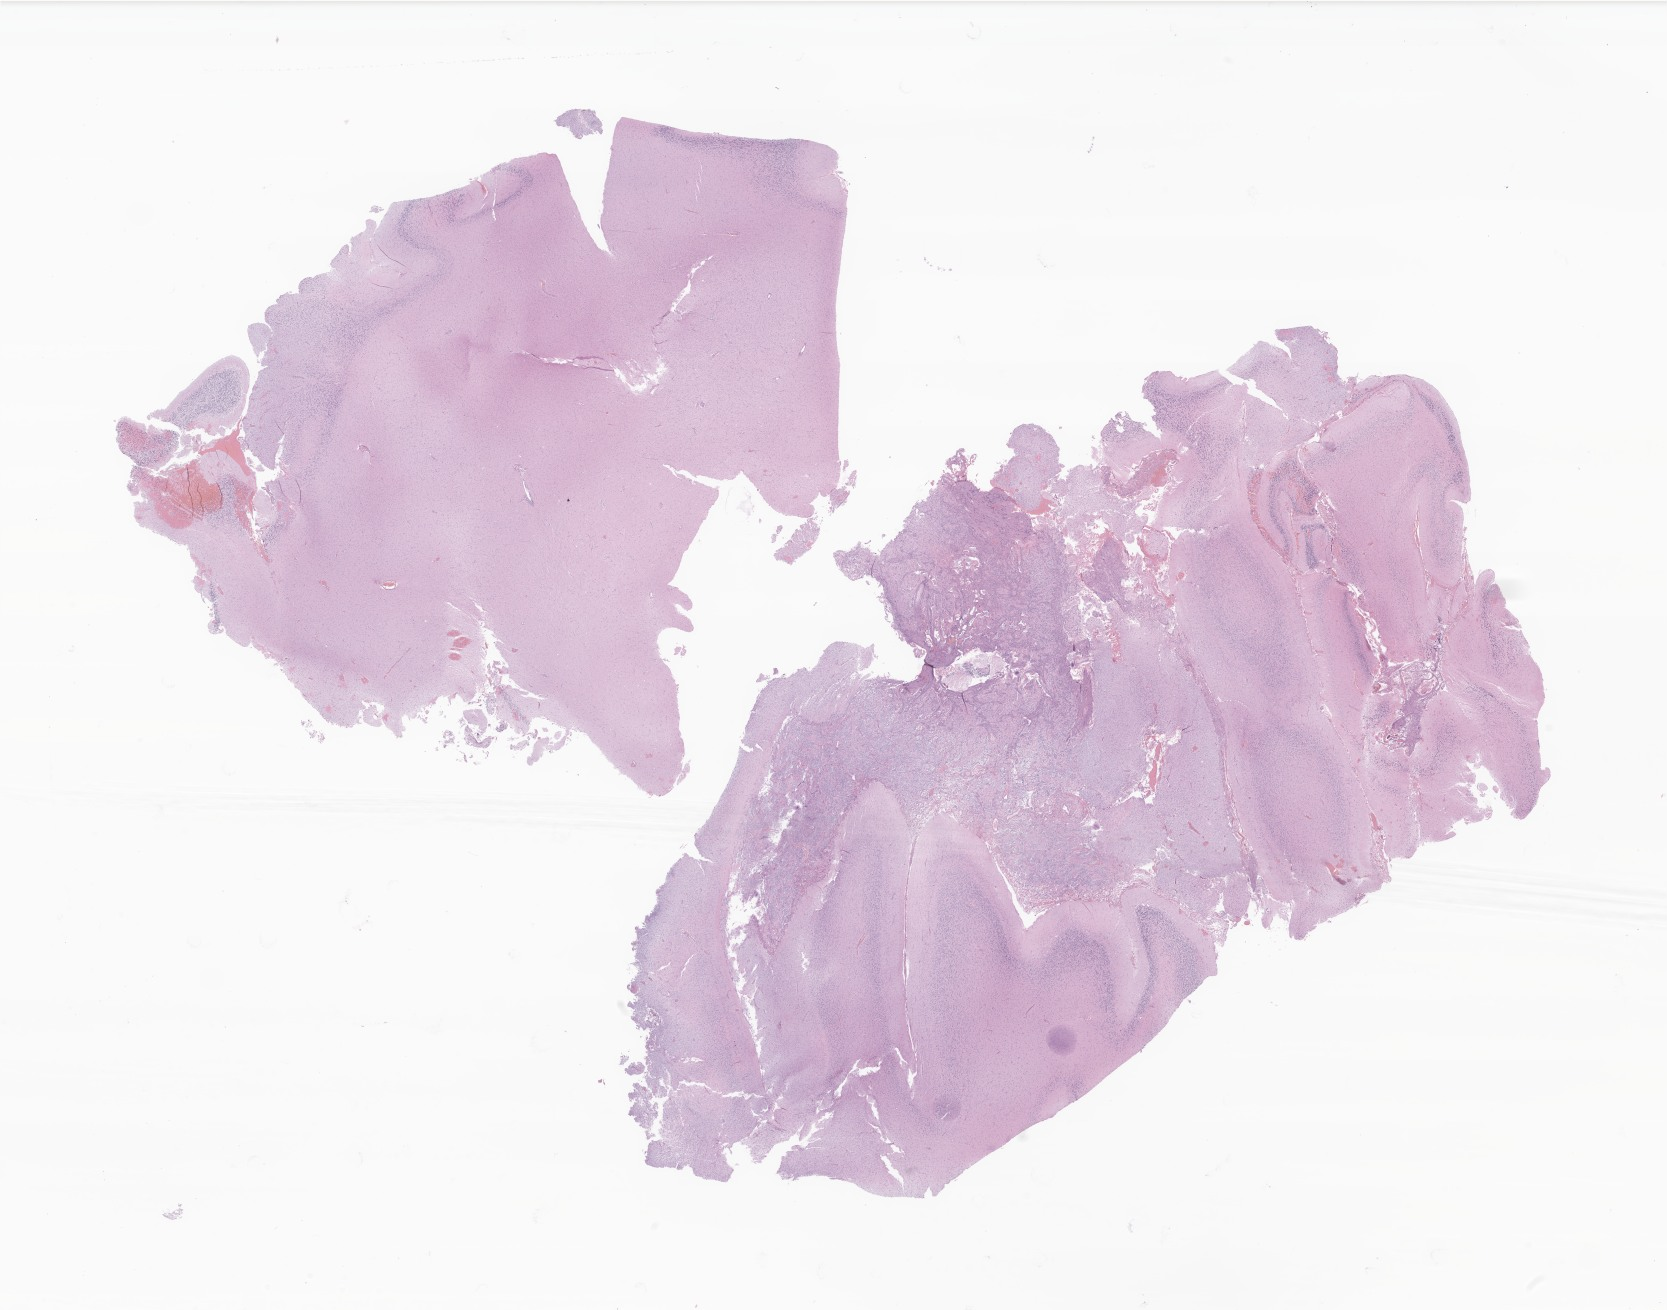
Digitized hematoxylin and eosin (H&E)-stained section of tumor tissue from the brain, shown as a low-resolution overview of the whole scanned area (about 28.1 x 22.1 mm), FFPE section. Male patient, age 661 days (about 1.8 years).
Recorded diagnosis: Neoplasm, uncertain whether benign or malignant.